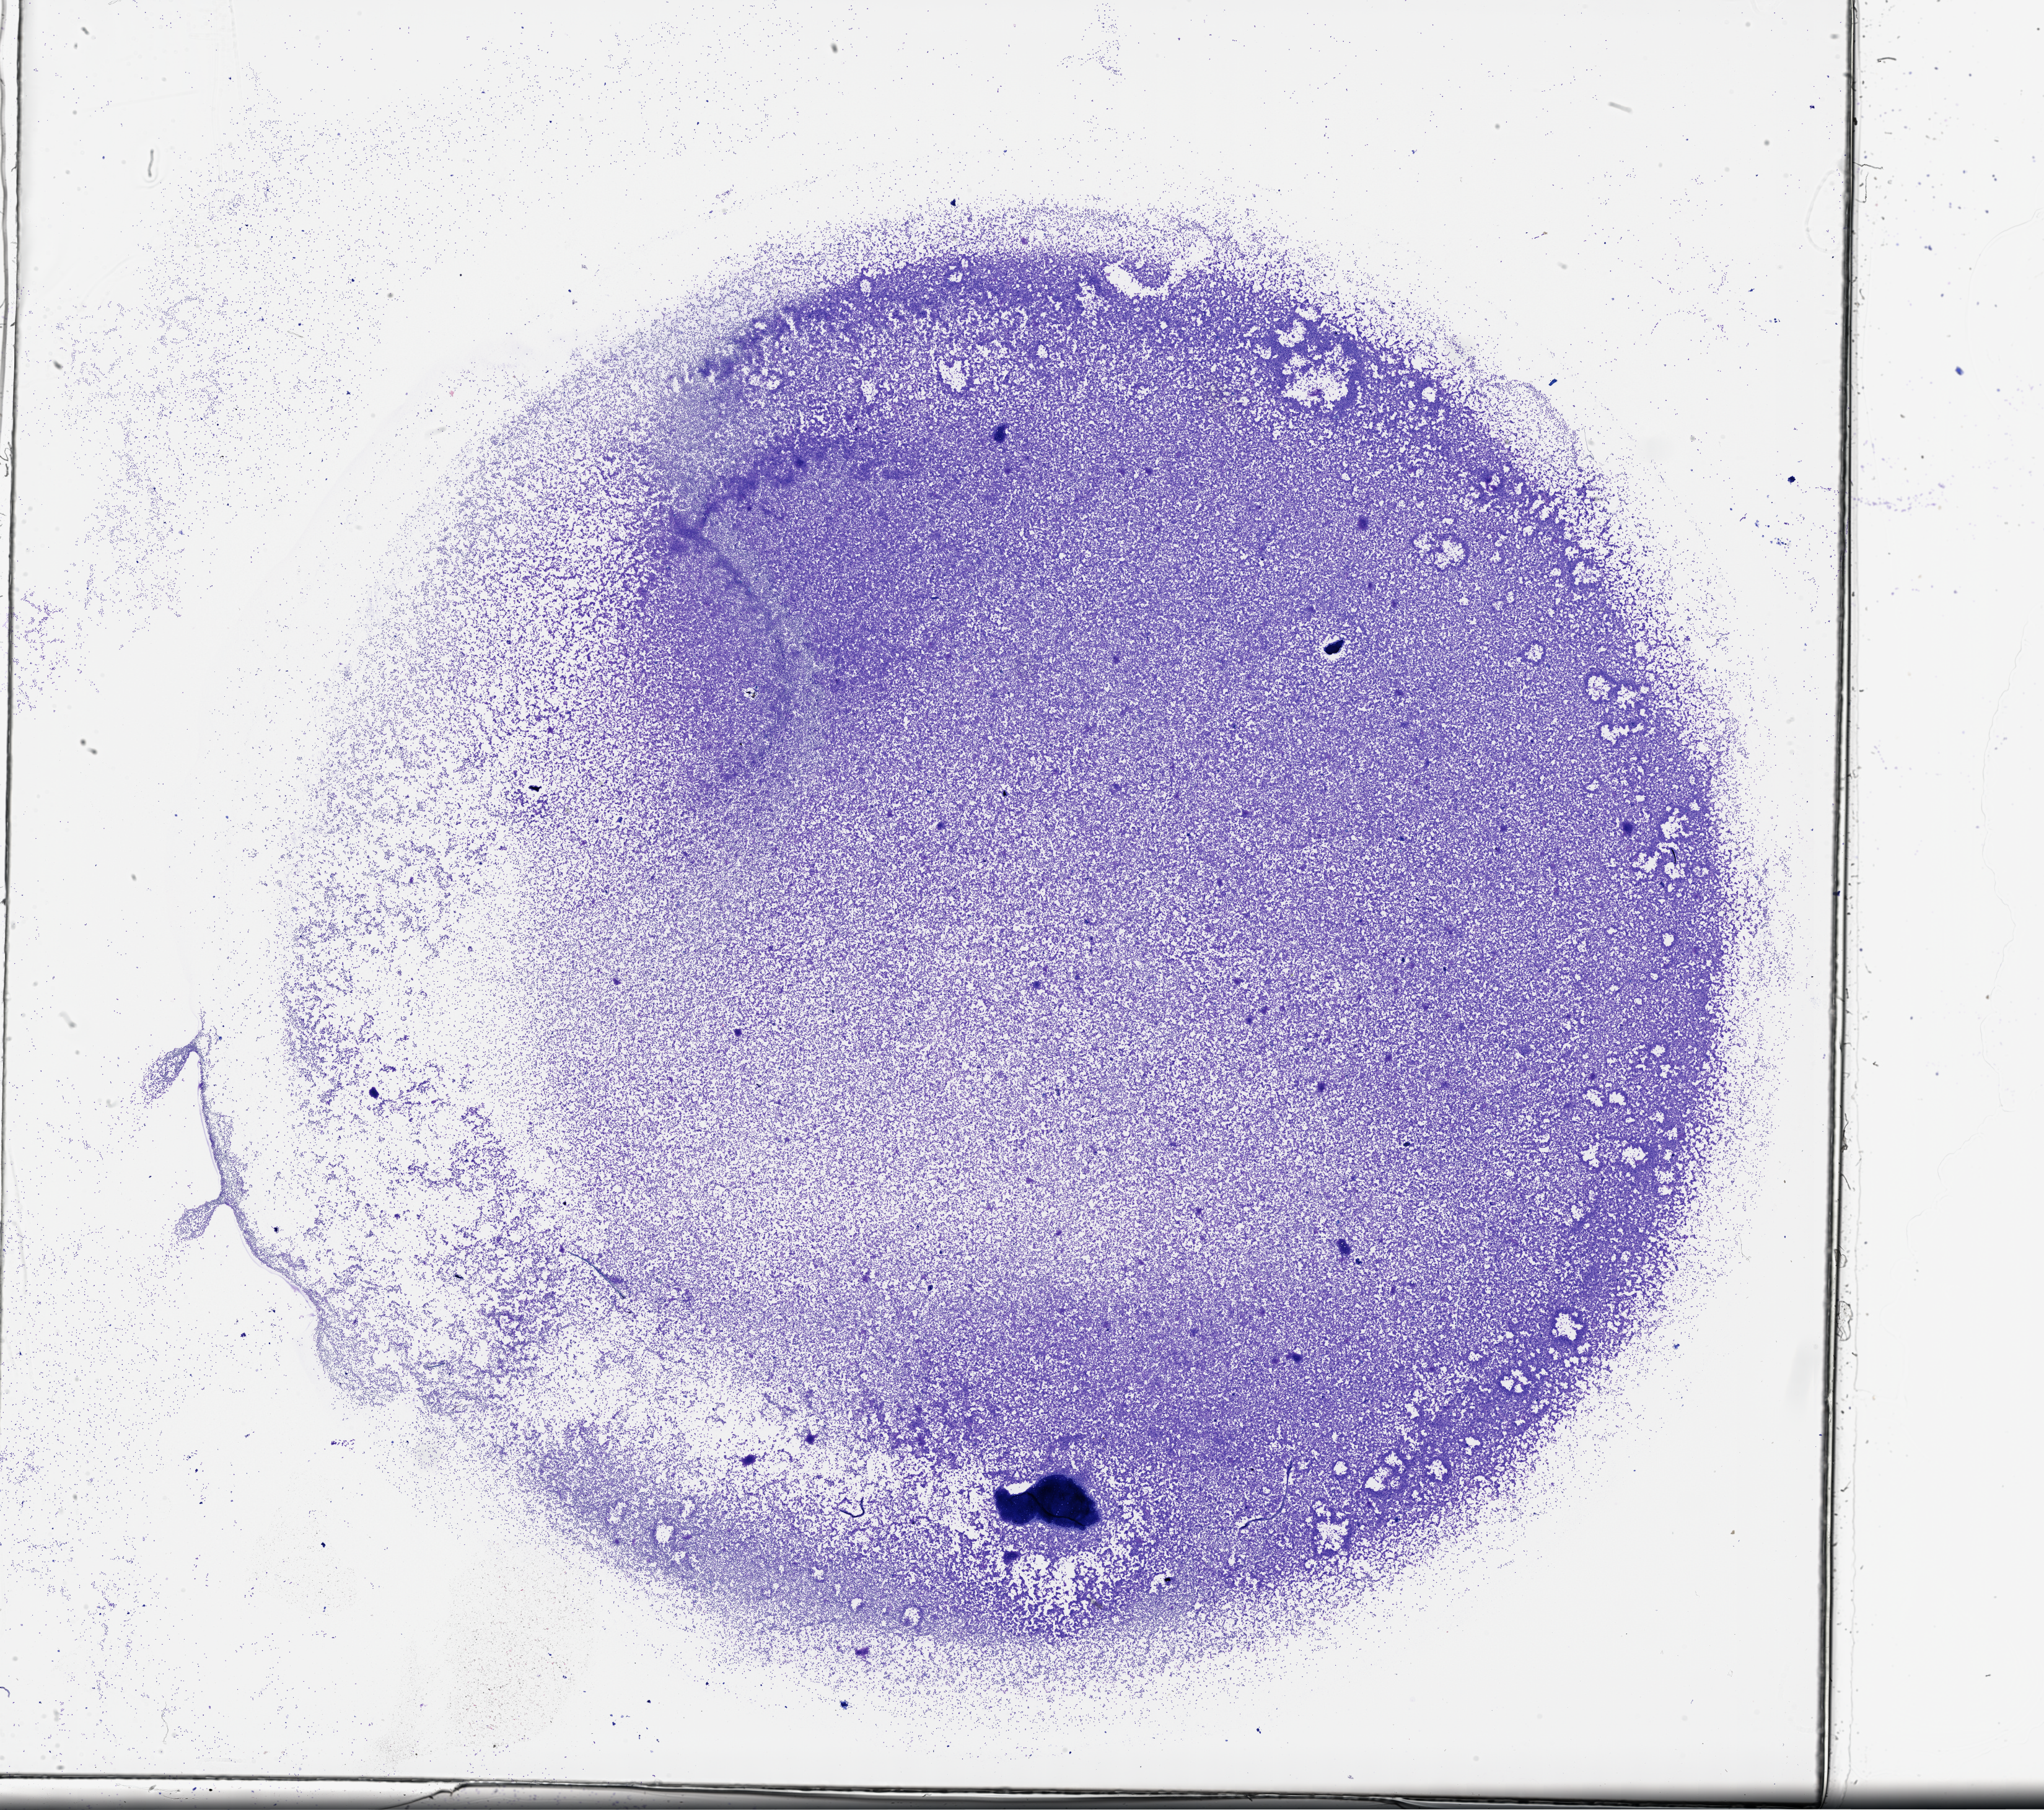
Digitized H&E-stained tissue section (whole slide) — shown as a low-resolution overview of the whole scanned area (about 26.6 x 23.6 mm, from a 40x scan); bone marrow (leukaemic) sample. Patient: female, age 42 years. Blasts: 80%.
Diagnosis: Acute Myeloid Leukemia. WHO classification: AML without maturation. FAB classification: M1.